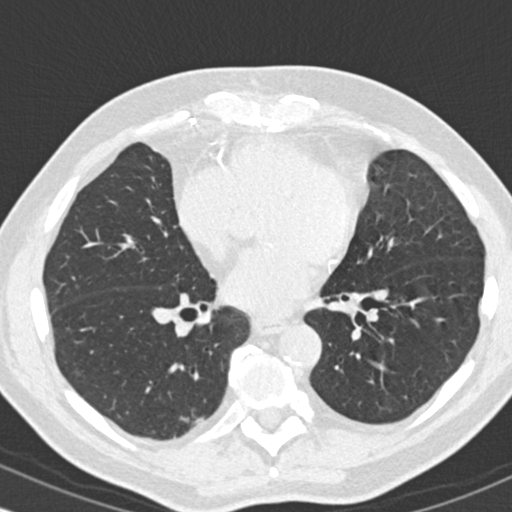
Chest CT (low-dose screening protocol), one axial image. Second annual screen. Lung window (W 1500 / L -600 HU). 120 kVp. Male, age 68 years at enrolment. Former smoker at enrolment.
Lesion marked by an expert reader, bounding box <166,401,216,446> (left, top, right, bottom; pixels). The screening reader recorded 2 non-calcified nodules or masses ≥4 mm on this exam; which of them this box marks is not recorded. Official screen result: positive, no significant change: stable abnormalities potentially related to lung cancer, unchanged since the prior screening exam.